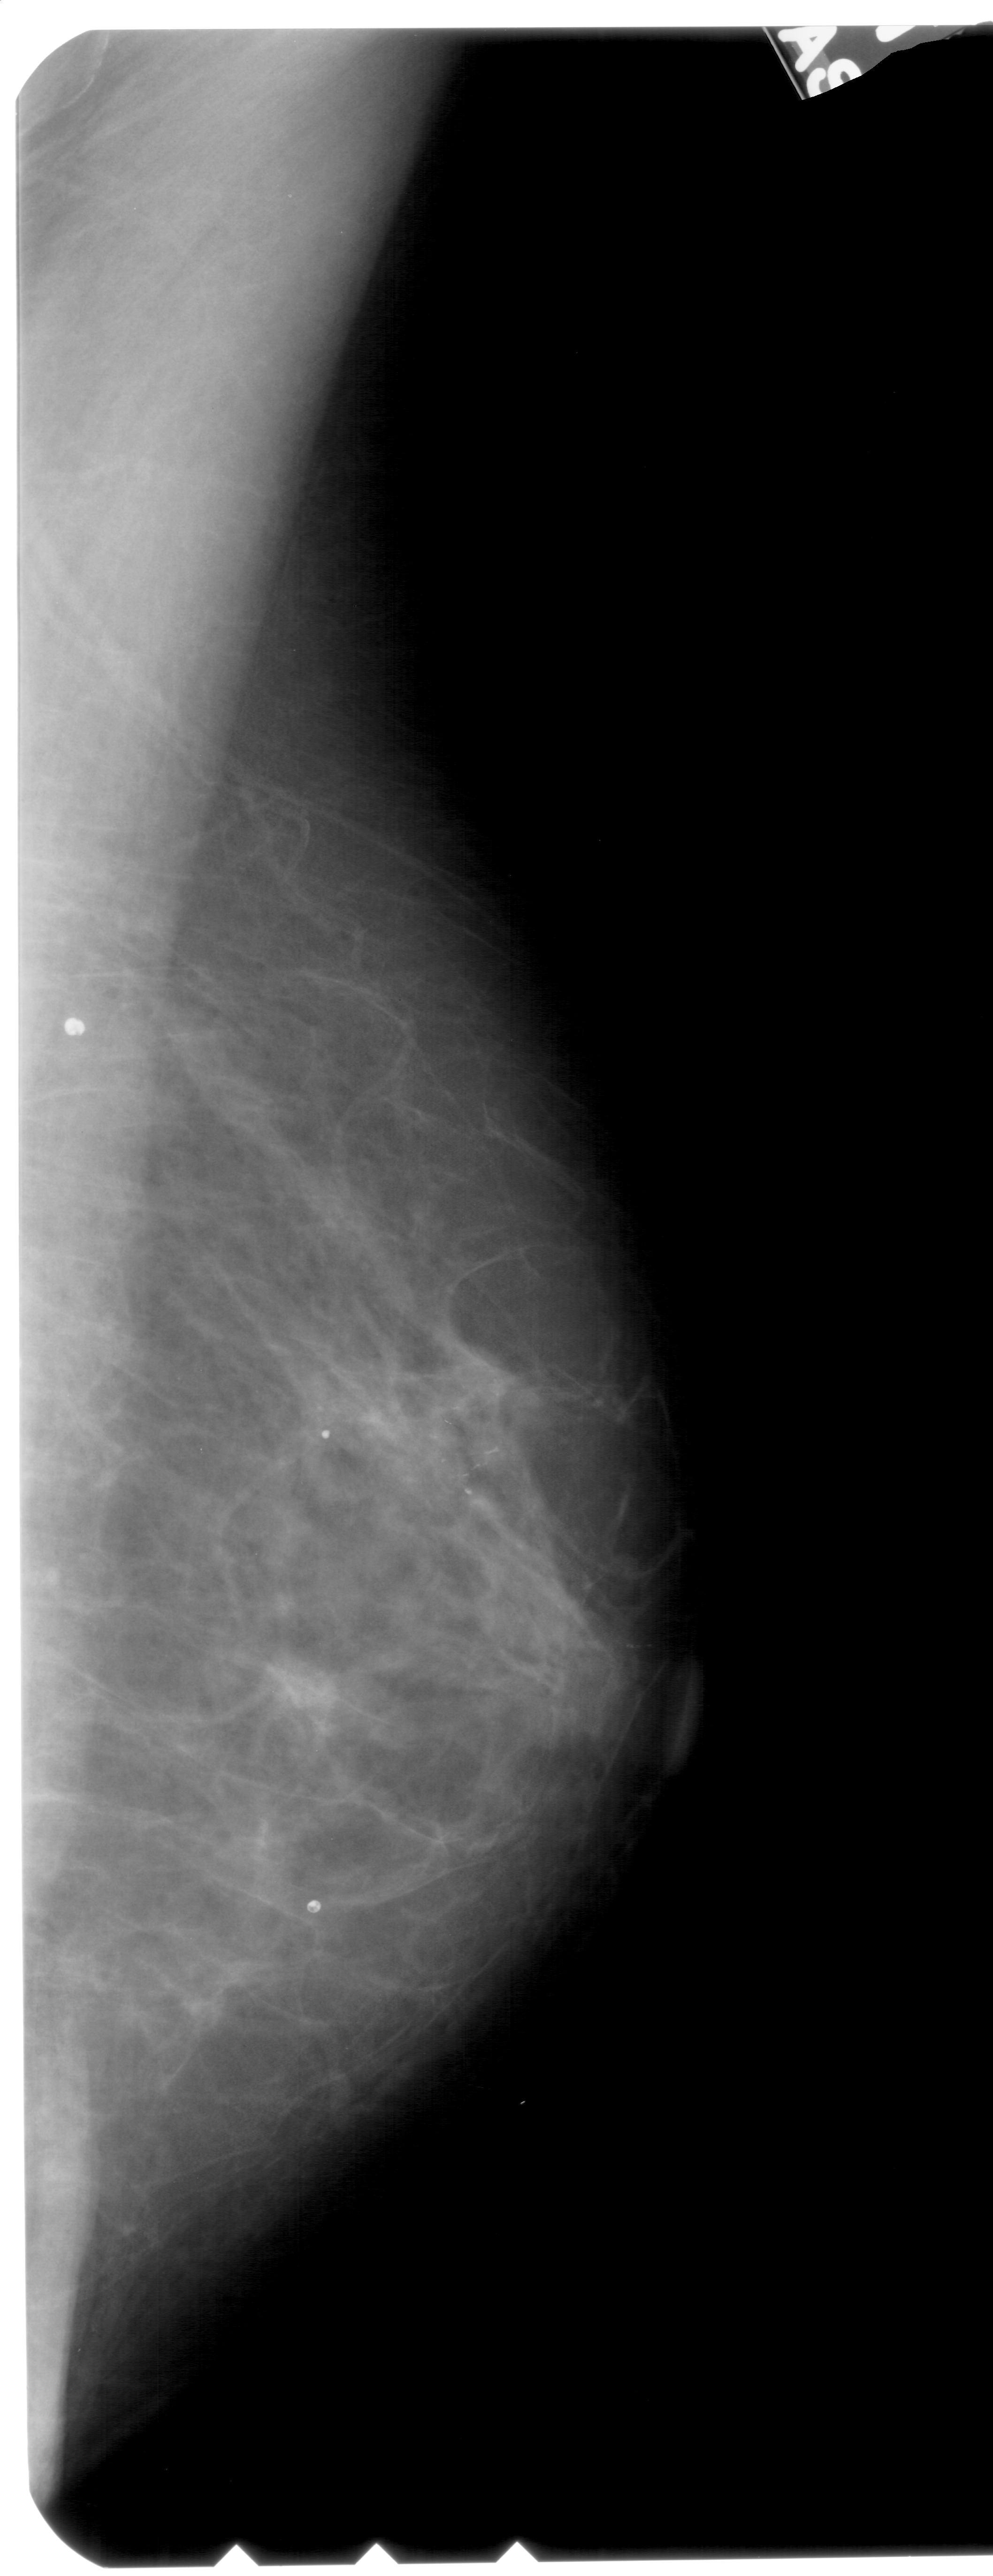
Mammogram (digitized film), right breast, MLO view.
Marked findings (only marked abnormalities are described; nothing is implied about the rest of the image): calcifications, morphology pleomorphic, distribution clustered; BI-RADS assessment category 4; subtlety rating 2 on a 1 (subtle) to 5 (obvious) scale; pathology result (as recorded, not read from the image): malignant.